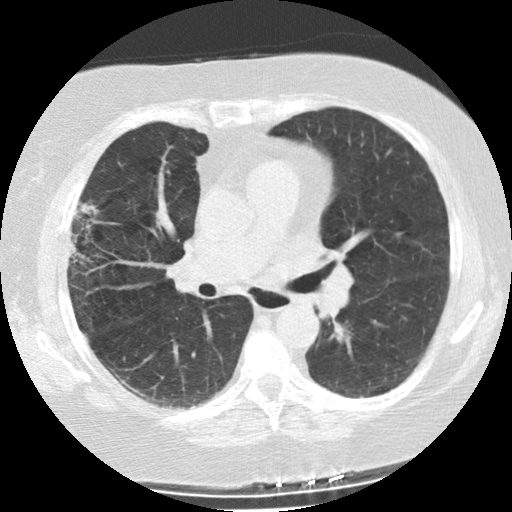
Chest CT (low-dose screening protocol), one axial image; second annual screen; lung window (W 1500 / L -600 HU); 2.5 mm slice thickness; slice 96 of 225 in the series. Female, age 73 years at enrolment. Former smoker at enrolment.
- Expert-annotated lung lesion, bounding box <57,197,104,274> (left, top, right, bottom; pixels).
- The screening reader recorded 2 non-calcified nodules or masses ≥4 mm on this exam; which of them this box marks is not recorded.
- Official screen result: positive, change unspecified: nodule(s) >= 4 mm or enlarging nodule(s), mass(es), or other non-specific abnormalities suspicious for lung cancer.
- Participant outcome: lung cancer diagnosed 47 days after this screen — bronchiolo-alveolar adenocarcinoma, NOS, right upper lobe, moderately differentiated (G2), stage IIIB (AJCC 6th edition), 21 mm at pathology.